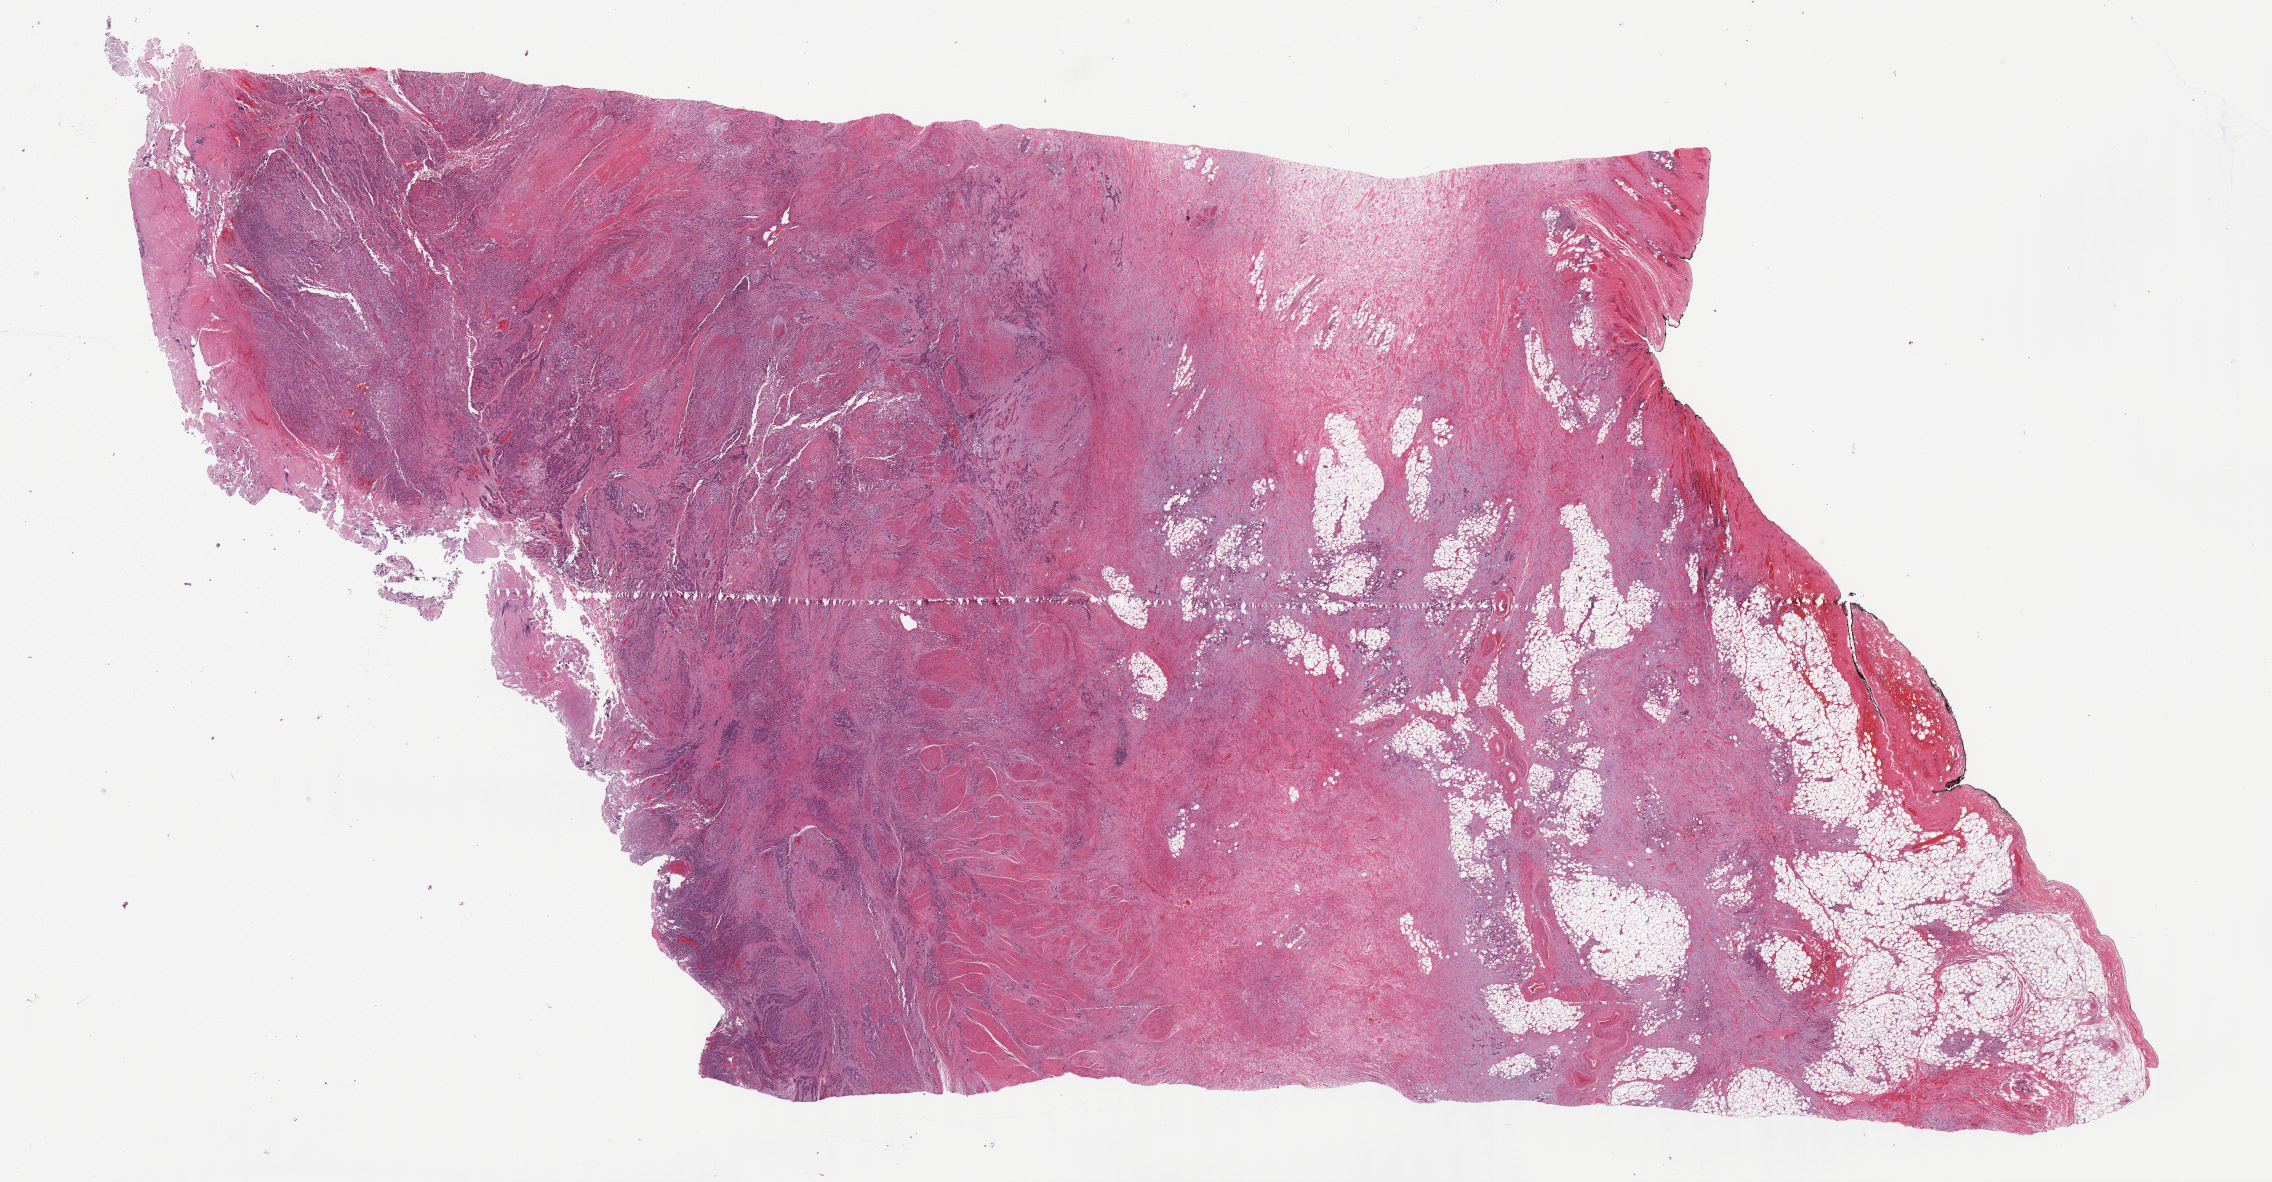
Digitized H&E-stained tissue section (whole slide), whole scanned area (about 36.7 x 19.1 mm, acquisition: 40x scan) shown as a low-resolution overview, FFPE section, bladder, primary tumour sample. Female patient; age at initial diagnosis 47 years.
Diagnosis: Transitional cell carcinoma.